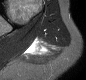
MRI of an extremity soft-tissue mass, one axial slice; slice 18 of 30 in the series (ordered by position); STIR; MR volume resampled by the dataset authors to the PET/CT grid (not the native acquisition matrix); 3.27 mm slice thickness; 86 × 80 image matrix, field of view 84 × 78 mm. Female patient. From the clinical record (not read from this slice): histological type: malignant fibrous histiocytoma; grade: low; site of the primary tumour: left arm.
Outlined on this slice (expert contour drawn on MRI and transferred to this co-registered scan by the dataset authors):
- gross tumour volume (mass): bounding box <26,38,48,55> (left, top, right, bottom; pixels)